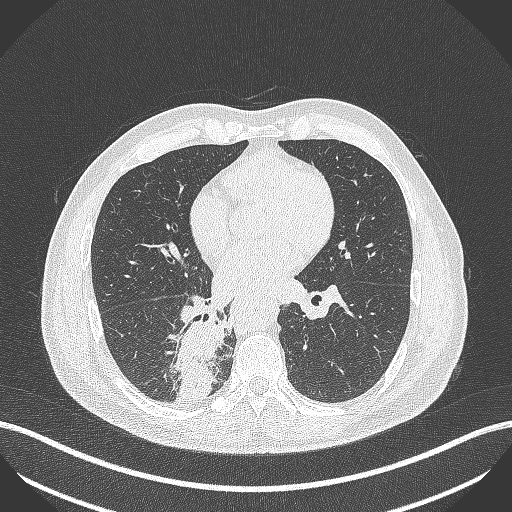
Chest CT, one axial slice; position 220 of 451 along the scan axis; reconstruction kernel B70f; lung window (W 1500 / L -600 HU); 1 mm slice thickness; 512 × 512 image matrix. Male patient, age 61 years. Case-level facts recorded for this patient, not image findings: clinical TNM (as recorded): T1 N0 M0.
Structures marked on this image (bounding box drawn by a radiologist):
- lung tumour (recorded histology: small cell carcinoma): box from (x=175, y=315) to (x=226, y=404) px